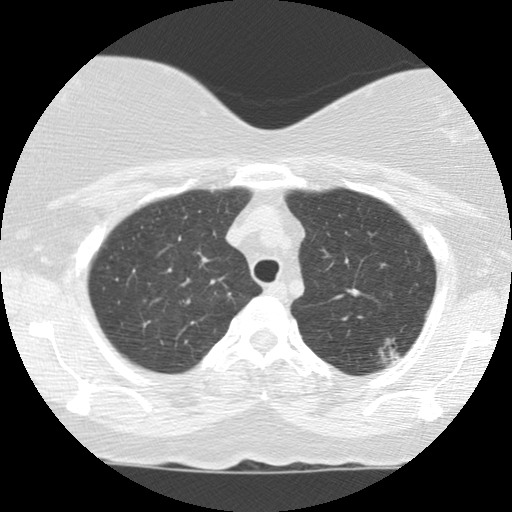
Chest CT (low-dose screening protocol), one axial image, baseline annual screen, lung window (W 1500 / L -600 HU), standard (soft-tissue) reconstruction kernel (STANDARD), 512 × 512 image matrix, field of view 310 × 310 mm. Female participant, aged 56 years at enrolment. Current smoker at enrolment.
Expert-annotated lung lesion, bounding box [x1, y1, x2, y2] px = [356, 319, 419, 384]. The screening reader recorded 4 non-calcified nodules or masses ≥4 mm on this exam; which of them this box marks is not recorded.